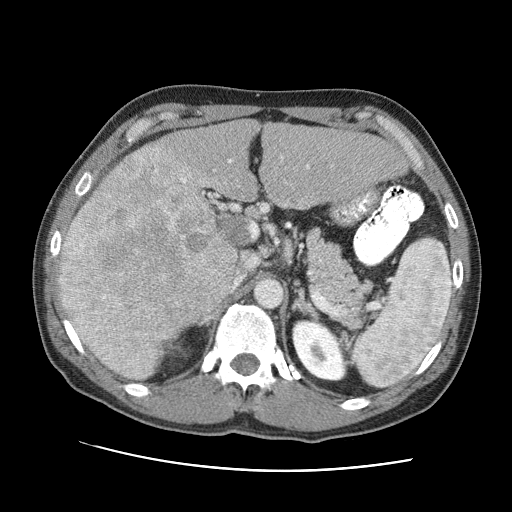
Contrast-enhanced abdominal CT (liver protocol), one axial slice; 120 kVp; one of 2 acquisitions stored at this slice position; soft-tissue window (W 400 / L 40 HU); 512 × 512 image matrix, field of view 360 × 360 mm. From the clinical record (not read from this slice): diagnosis: hepatocellular carcinoma (patient treated with transarterial chemoembolisation; whether this scan precedes or follows treatment is not stated here); TNM stage (as recorded): Stage-IVA; Child-Pugh class: A; tumour nodularity: multinodular.
Structures marked on this image (semi-automatic segmentation, software-assisted and operator-edited):
- abdominal aorta: bounding box <256,280,282,307> (left, top, right, bottom; pixels)
- liver parenchyma outside the tumour (the mass and vessels are separate outlines, so this box may not span the whole liver): <60,120,406,378>
- mass: <57,138,251,377>
- liver vessels: <69,156,310,331>